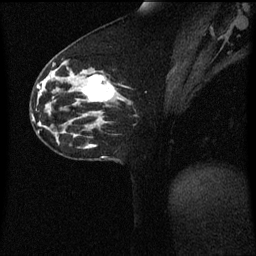
Breast MRI (dynamic contrast-enhanced), one sagittal slice; slice 29 of 60 in the series (ordered by position); dynamic contrast-enhanced series, image 2 of 3 at this slice position (ordered by acquisition); 1.5 T; TE 4.2 ms, TR 8.4 ms; 2 mm slice thickness; 256 × 256 image matrix. Patient: female, 33 years. From the clinical record (not read from this slice): setting: breast cancer imaged before/during neoadjuvant chemotherapy; receptor status: triple-negative.
Structures marked on this image (semi-automatically segmented with operator editing):
- analysis volume of interest (the breast-tissue region the enhancement analysis was run in; not a lesion): bounding box (x1, y1, x2, y2) in pixels: (76, 68, 123, 113)
- tumour enhancement mask (voxels above the 70 % enhancement threshold inside the analysis volume of interest): (81, 74, 114, 103)